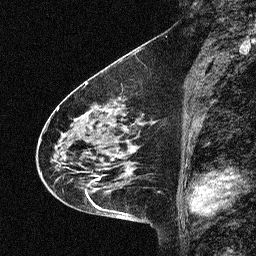
Breast MRI (dynamic contrast-enhanced), one sagittal slice; position 26 of 64 along the scan axis; dynamic contrast-enhanced study with each time point stored as its own series, time point 2 of 3 at this slice position (early post-contrast, ordered by acquisition time); 1.5 T; TE 4.5 ms, TR 11 ms; 2.06 mm slice thickness; 256 × 256 image matrix, field of view 200 × 200 mm. Female patient, age 46 years. Case-level facts recorded for this patient, not image findings: setting: breast cancer imaged before/during neoadjuvant chemotherapy; receptor status: HER2-positive.
Outlined on this slice (semi-automatic segmentation, software-assisted and operator-edited):
- analysis volume of interest (the breast-tissue region the enhancement analysis was run in; not a lesion): bounding box (x1, y1, x2, y2) in pixels: (42, 80, 150, 180)
- tumour enhancement mask (voxels above the 90 % enhancement threshold inside the analysis volume of interest): (52, 115, 139, 179)